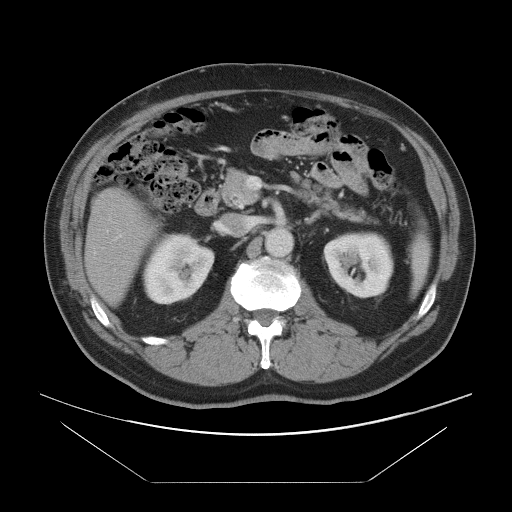
Contrast-enhanced abdominal CT, one axial slice; slice 43 of 97 in the series (ordered by position); intravenous contrast given; soft-tissue window (W 400 / L 40 HU); 512 × 512 image matrix, field of view 442 × 442 mm. Male patient, age 62 years. Case-level facts recorded for this patient, not image findings: diagnosis: colorectal cancer liver metastases, imaged before liver resection; multiple liver metastases: no; largest metastasis: 7 cm; disease in both lobes: yes.
Annotated regions visible in this slice (expert manual segmentation):
- hepatic veins: box from (x=106, y=230) to (x=109, y=233) px
- liver: (x=87, y=189)–(x=153, y=303)
- planned liver remnant (the part of the liver to remain after resection): (x=86, y=189)–(x=154, y=303)
- portal vein (with intrahepatic branches): (x=118, y=235)–(x=121, y=237)